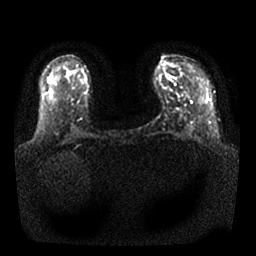
Breast MRI, one axial slice; position 14 of 25 along the scan axis; diffusion-weighted series; image 2 of 4 stored at this slice position (different b-values; order by instance number); 1.5 T; 4 mm slice thickness; 256 × 256 image matrix, field of view 340 × 340 mm. Female patient.
Annotated regions visible in this slice (manually delineated by an expert):
- tumour on diffusion-weighted imaging: bounding box (x1, y1, x2, y2) in pixels: (80, 75, 86, 80)